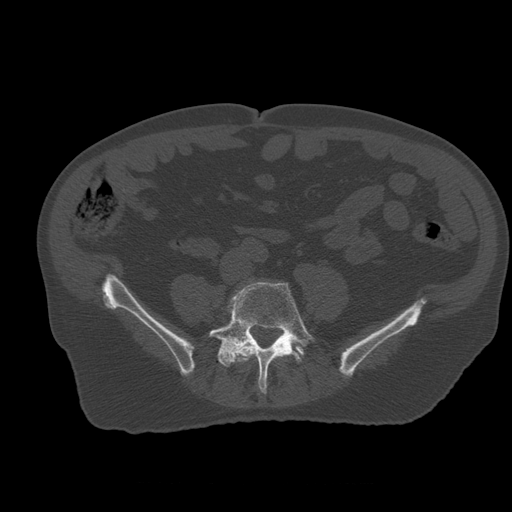
CT including the spine, one axial slice; position 145 of 399 along the scan axis; bone window (W 1800 / L 400 HU); 1.25 mm slice thickness; 512 × 512 image matrix, field of view 407 × 407 mm. Patient age 73 years. Case-level facts recorded for this patient, not image findings: primary cancer: prostate; vertebrae with lytic lesions (as recorded): L2.
Annotated regions visible in this slice (semi-automatically segmented with operator editing):
- L4 vertebra: bounding box <235,343,259,363> (left, top, right, bottom; pixels)
- L5 vertebra: <209,282,316,394>